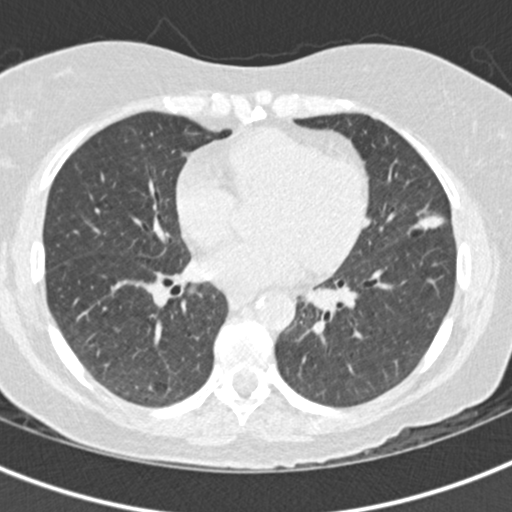
Low-dose screening chest CT, one axial slice; slice 79 of 156 in the series (ordered by position); lung window (W 1500 / L -600 HU); 2 mm slice thickness; 512 × 512 image matrix, field of view 298 × 298 mm.
Annotated regions visible in this slice (outlined manually by an expert reader):
- lesion 1 (tumor, lingular bronchus): bounding box [x1, y1, x2, y2] px = [414, 210, 444, 230]